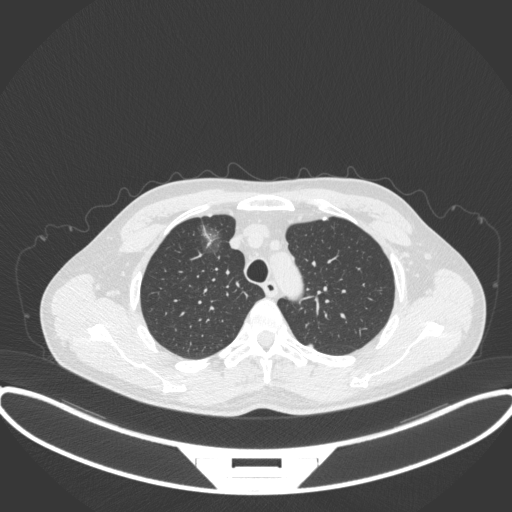
Chest CT, one axial slice; position 287 of 395 along the scan axis; lung window (W 1500 / L -600 HU); 512 × 512 image matrix. Patient: male, 60 years. Case-level facts recorded for this patient, not image findings: clinical TNM (as recorded): T1c N0 M0.
Outlined on this slice (rectangle marked by the reading radiologist):
- lung tumour (recorded histology: adenocarcinoma): bounding box <192,218,227,259> (left, top, right, bottom; pixels)